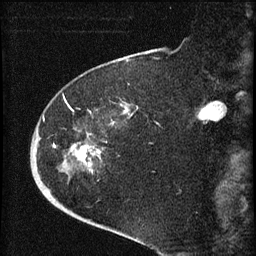
Breast MRI (dynamic contrast-enhanced), one sagittal slice; dynamic contrast-enhanced series, image 2 of 4 at this slice position (ordered by acquisition); 1.5 T; TE 4.2 ms, TR 8.2 ms; 2 mm slice thickness; 256 × 256 image matrix, field of view 180 × 180 mm. Female patient, age 71 years.
Annotated regions visible in this slice (semi-automatically segmented with operator editing):
- analysis volume of interest (the breast-tissue region the enhancement analysis was run in; not a lesion): box from (x=35, y=75) to (x=133, y=190) px
- tumour enhancement mask (voxels above the 70 % enhancement threshold inside the analysis volume of interest): (x=54, y=122)–(x=114, y=167)